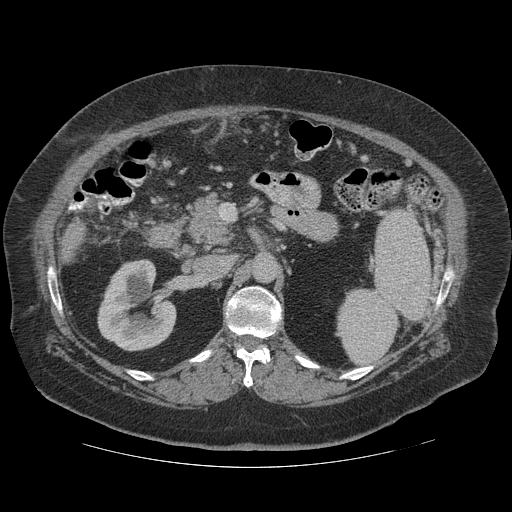
Contrast-enhanced abdominal CT (liver protocol), one axial slice. Slice 54 of 121 in the series (ordered by position). Reconstruction kernel STANDARD. 140 kVp. Soft-tissue window (W 400 / L 40 HU). 512 × 512 image matrix, field of view 420 × 420 mm. Case-level facts recorded for this patient, not image findings: diagnosis: hepatocellular carcinoma (patient treated with transarterial chemoembolisation; whether this scan precedes or follows treatment is not stated here); TNM stage (as recorded): Stage-IIIA; Child-Pugh class: A; tumour differentiation: well differentiated; tumour size: 7.4 cm.
Outlined on this slice (semi-automatic segmentation, software-assisted and operator-edited):
- liver parenchyma outside the tumour (the mass and vessels are separate outlines, so this box may not span the whole liver): box from (x=60, y=219) to (x=84, y=262) px